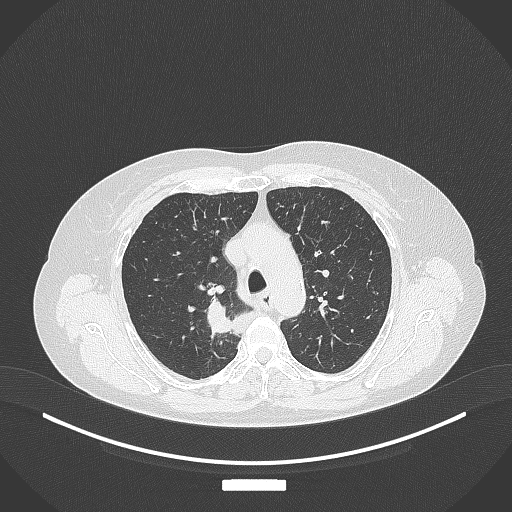
Chest CT, one axial slice; slice 278 of 357 in the series (ordered by position); 120 kVp; lung window (W 1500 / L -600 HU); 512 × 512 image matrix, field of view 400 × 400 mm. Patient: female, 62 years. From the clinical record (not read from this slice): clinical TNM (as recorded): T1c N1 M0.
Structures marked on this image (bounding box drawn by a radiologist):
- lung tumour (recorded histology: squamous cell carcinoma): bounding box [x1, y1, x2, y2] px = [205, 299, 247, 344]